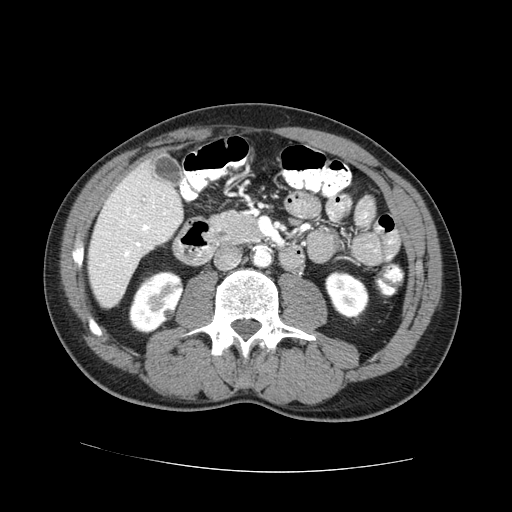
Contrast-enhanced abdominal CT (liver protocol), one axial slice; position 19 of 73 along the scan axis; reconstruction kernel STANDARD; 100 kVp; one of 2 acquisitions stored at this slice position; soft-tissue window (W 400 / L 40 HU); 2.5 mm slice thickness; 512 × 512 image matrix, field of view 380 × 380 mm. Case-level facts recorded for this patient, not image findings: diagnosis: hepatocellular carcinoma (patient treated with transarterial chemoembolisation; whether this scan precedes or follows treatment is not stated here); TNM stage (as recorded): Stage-IVA; Child-Pugh class: A; tumour differentiation: no biopsy; tumour nodularity: uninodular.
Outlined on this slice (semi-automatic segmentation, software-assisted and operator-edited):
- liver parenchyma outside the tumour (the mass and vessels are separate outlines, so this box may not span the whole liver): bounding box (x1, y1, x2, y2) in pixels: (88, 152, 182, 308)
- liver vessels: (121, 206, 154, 257)